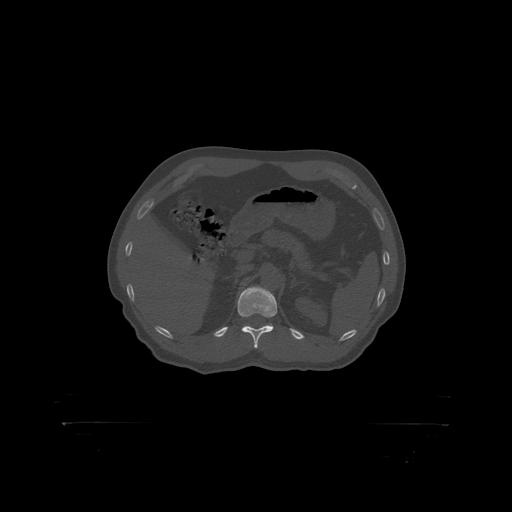
CT including the spine, one axial slice. Position 347 of 399 along the scan axis. 120 kVp. Bone window (W 1800 / L 400 HU). 1.25 mm slice thickness. 512 × 512 image matrix, field of view 650 × 650 mm. Male patient, age 46 years. From the clinical record (not read from this slice): primary cancer: skin.
Structures marked on this image (semi-automatically segmented with operator editing):
- T12 vertebra: bounding box <238,287,277,318> (left, top, right, bottom; pixels)